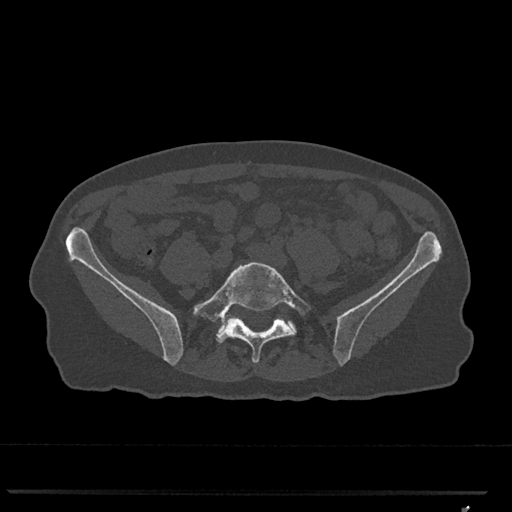
CT including the spine, one axial slice. Slice 147 of 793 in the series (ordered by position). 120 kVp. Bone window (W 1800 / L 400 HU). 512 × 512 image matrix, field of view 380 × 380 mm. Female patient, age 62 years. Case-level facts recorded for this patient, not image findings: primary cancer: renal.
Outlined on this slice (semi-automatic segmentation, software-assisted and operator-edited):
- L5 vertebra: bounding box [x1, y1, x2, y2] px = [193, 262, 313, 363]